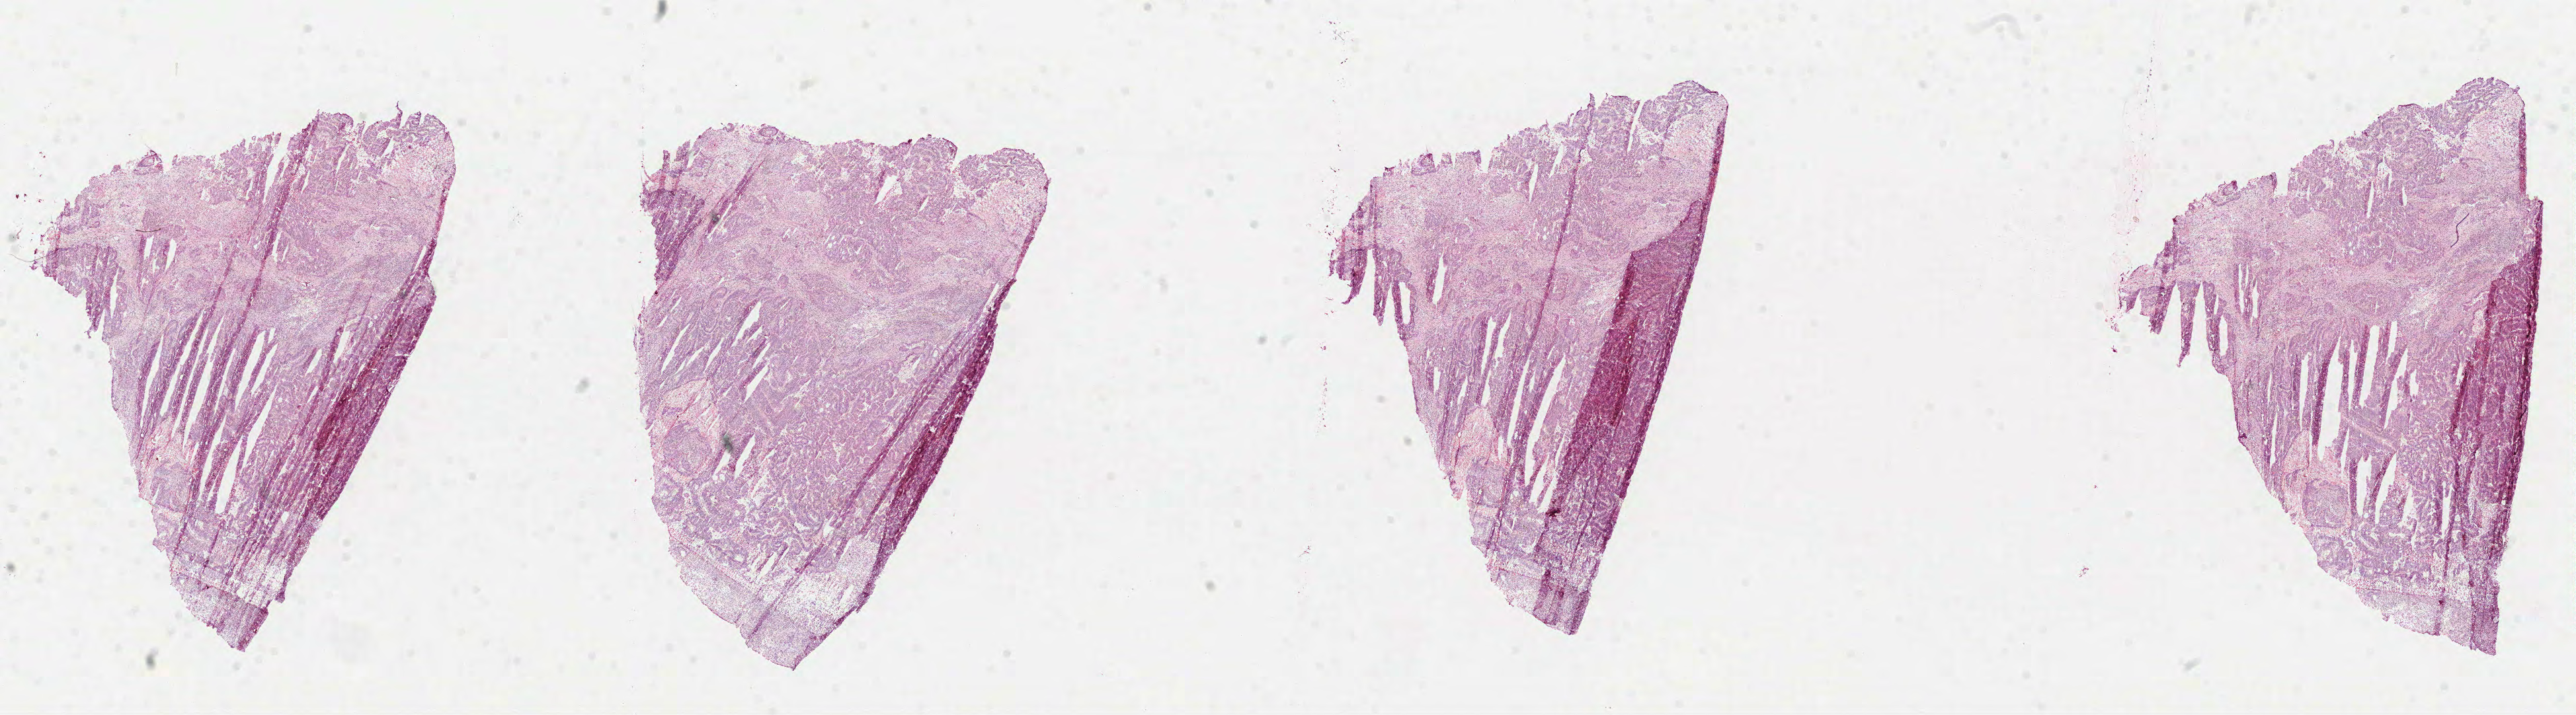
Hematoxylin and eosin (H&E) stained whole-slide image — shown as a low-resolution overview of the whole scanned area (about 31.4 x 8.7 mm), formalin-fixed paraffin-embedded (FFPE) diagnostic section, sample: primary tumour, colon. Male, age 68 years at initial diagnosis.
Histologic diagnosis: Adenocarcinoma, NOS (sigmoid colon).